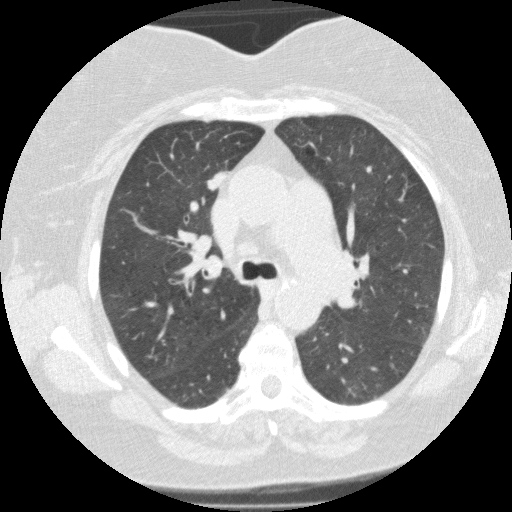
Low-dose screening chest CT, axial slice, third annual screen, lung window (W 1500 / L -600 HU), standard (soft-tissue) reconstruction kernel (FC01), 120 kVp. Female, age 62 years at enrolment.
Expert-annotated lung lesion, bounding box [x1, y1, x2, y2] px = [190, 161, 237, 200]. The screening reader recorded 5 non-calcified nodules or masses ≥4 mm on this exam (right upper lobe, right lower lobe, right lower lobe, right lower lobe, right lower lobe); which of them this box marks is not recorded. Participant outcome: lung cancer diagnosed 76 days after this screen — adenocarcinoma, NOS, right upper lobe, poorly differentiated (G3), stage IB (AJCC 6th edition), 12 mm at pathology.